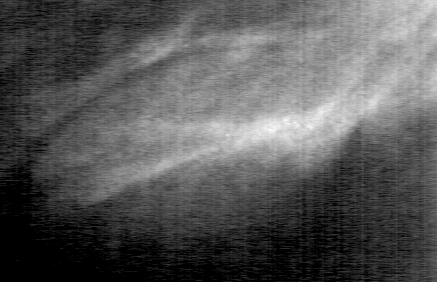
Region of interest cut from a scanned film mammogram (one marked finding), left breast, MLO view.
Finding: mass, shape oval, margins circumscribed; BI-RADS assessment category 3; subtlety rating 3 on a 1 (subtle) to 5 (obvious) scale; pathology result (as recorded, not read from the image): benign.